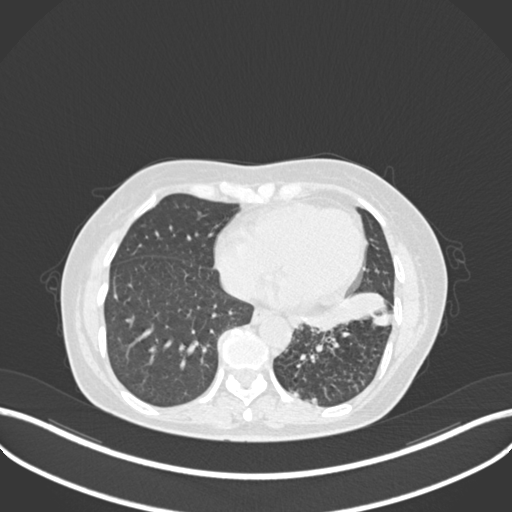
Chest CT, one axial slice; position 91 of 270 along the scan axis; lung window (W 1500 / L -600 HU); 1 mm slice thickness; 512 × 512 image matrix, field of view 400 × 400 mm. Patient: female, 63 years. From the clinical record (not read from this slice): clinical TNM (as recorded): T1b N0 M0.
Outlined on this slice (rectangle marked by the reading radiologist):
- lung tumour (recorded histology: adenocarcinoma): bounding box (x1, y1, x2, y2) in pixels: (301, 287, 390, 336)